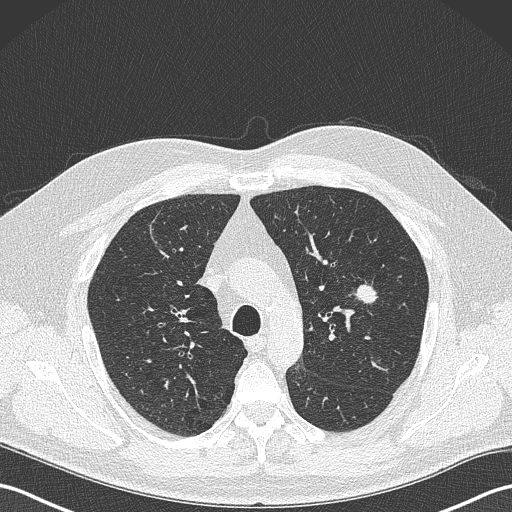
Chest CT (low-dose screening protocol), one axial image; baseline screening round; lung window (W 1500 / L -600 HU); slice 99 of 343 in the series; 512 × 512 image matrix. Male, age 61 years at enrolment. Former smoker at enrolment.
Expert-annotated lung lesion, bounding box <341,276,385,317> (left, top, right, bottom; pixels). The screening reader recorded 2 non-calcified nodules or masses ≥4 mm on this exam; which of them this box marks is not recorded. Lung cancer was diagnosed 160 days after this screen: adenocarcinoma, NOS, left upper lobe, poorly differentiated (G3), stage IA (AJCC 6th edition), 28 mm at pathology.